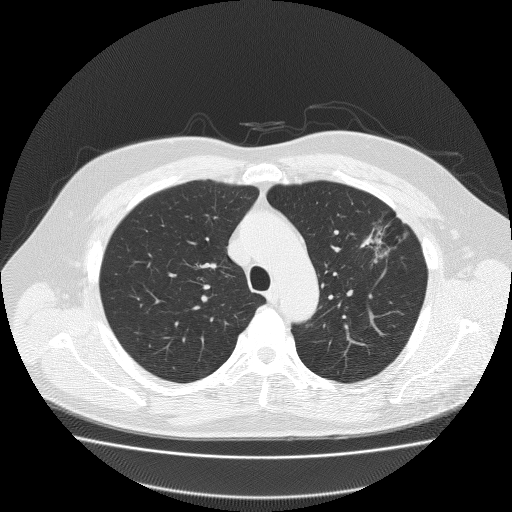
Low-dose screening chest CT, one axial slice. Slice 150 of 204 in the series (ordered by position). 120 kVp. Lung window (W 1500 / L -600 HU). 2 mm slice thickness. 512 × 512 image matrix.
Annotated regions visible in this slice (expert manual segmentation):
- lesion 1 (tumor, upper lobe of left lung): bounding box [x1, y1, x2, y2] px = [360, 224, 388, 249]